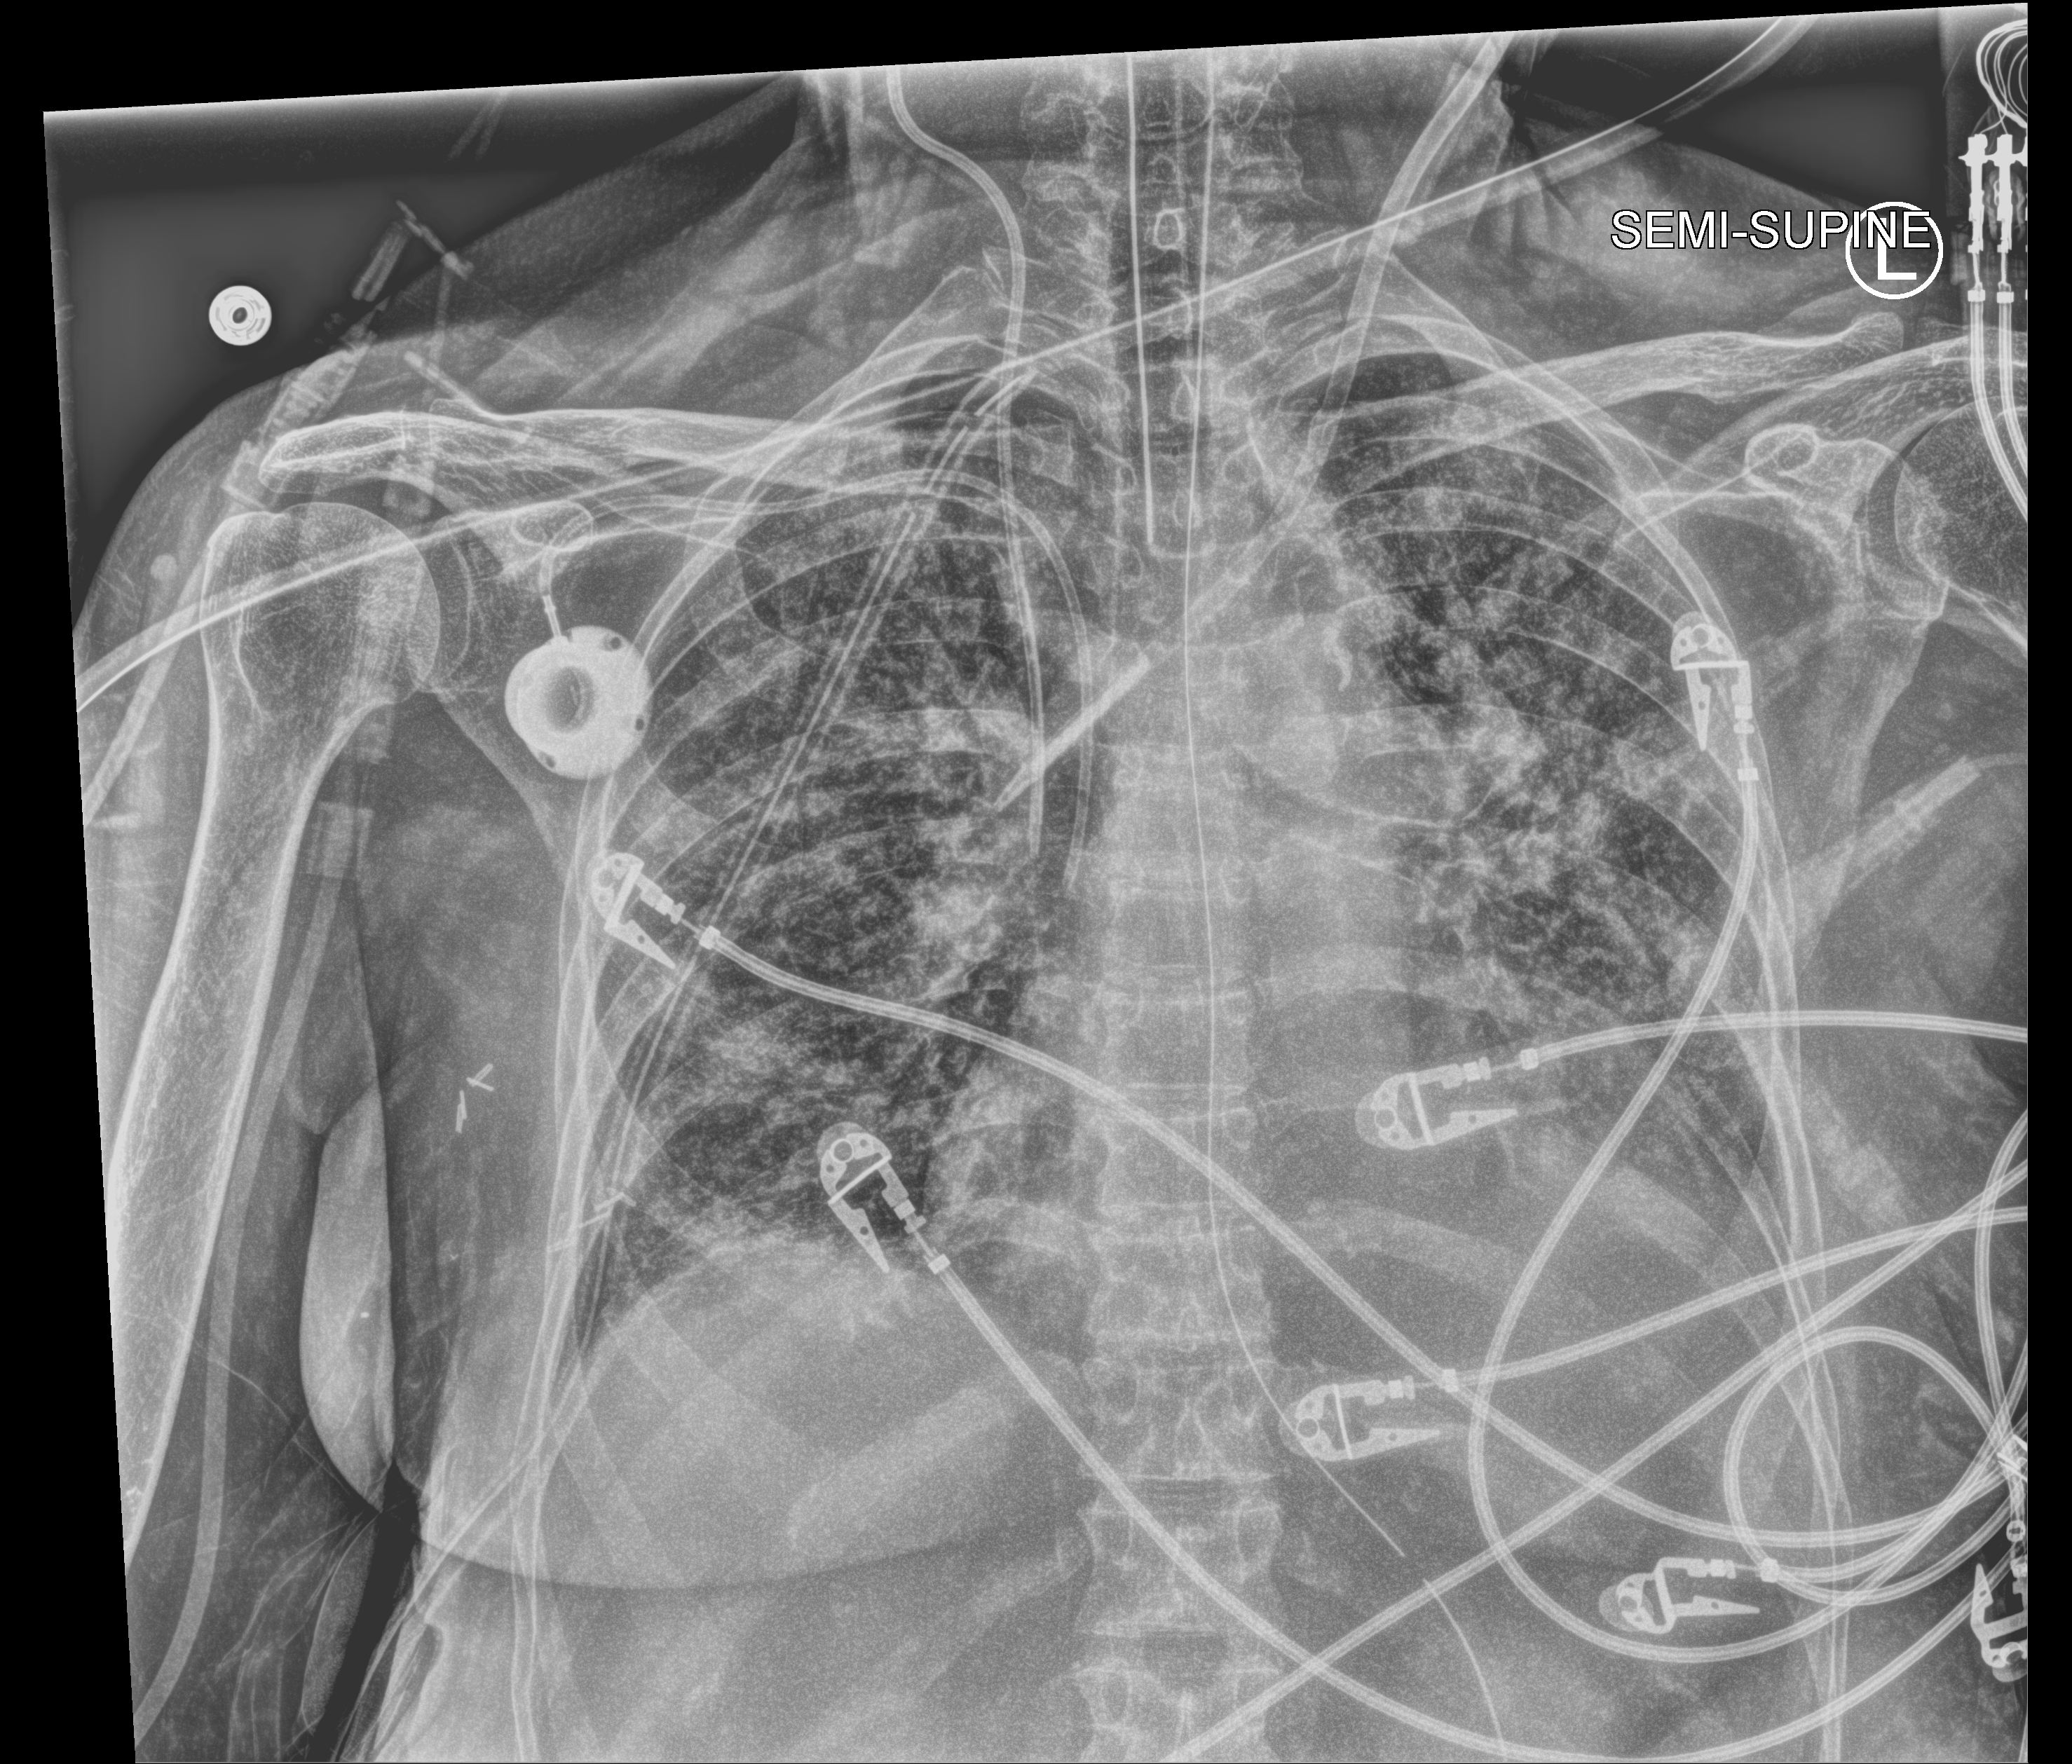
Portable chest radiograph; anteroposterior (AP) projection. Female patient hospitalised with COVID-19, age 60–74 years.
From the hospital-stay record, not from the radiograph (when in the stay this image was taken is not recorded): mechanically ventilated during this hospital stay: yes; admitted to intensive care during this hospital stay: yes.